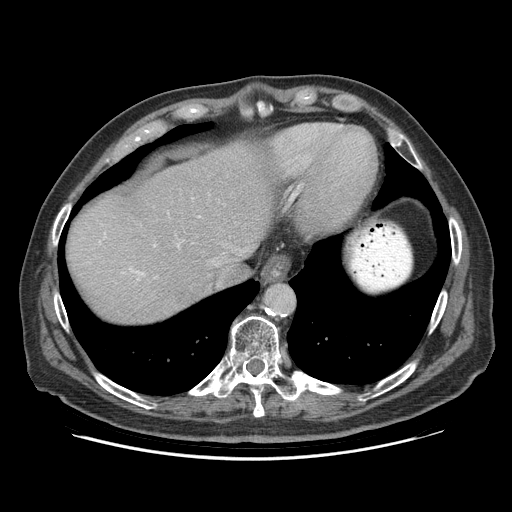
Contrast-enhanced abdominal CT (liver protocol), one axial slice; position 76 of 95 along the scan axis; reconstruction kernel STANDARD; 140 kVp; soft-tissue window (W 400 / L 40 HU); 2.5 mm slice thickness; 512 × 512 image matrix. Case-level facts recorded for this patient, not image findings: diagnosis: hepatocellular carcinoma (patient treated with transarterial chemoembolisation; whether this scan precedes or follows treatment is not stated here); TNM stage (as recorded): Stage-IVB; Child-Pugh class: A; tumour differentiation: well differentiated; tumour nodularity: uninodular.
Annotated regions visible in this slice (semi-automatically segmented with operator editing):
- abdominal aorta: bounding box <265,284,294,314> (left, top, right, bottom; pixels)
- liver parenchyma outside the tumour (the mass and vessels are separate outlines, so this box may not span the whole liver): <68,142,278,322>
- liver vessels: <130,269,142,274>